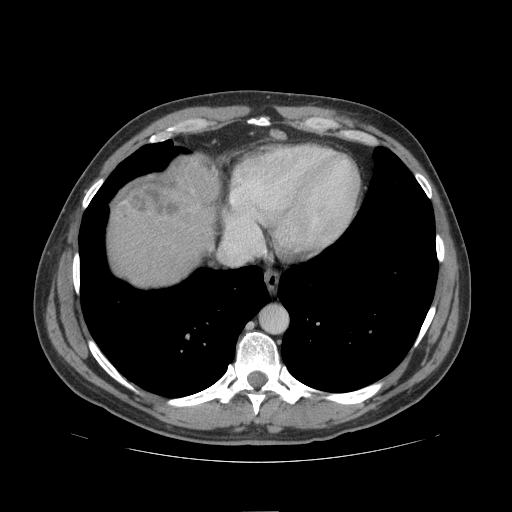
Contrast-enhanced abdominal CT (liver protocol), one axial slice; slice 94 of 109 in the series (ordered by position); reconstruction kernel STANDARD; soft-tissue window (W 400 / L 40 HU); 2.5 mm slice thickness; 512 × 512 image matrix, field of view 420 × 420 mm. Case-level facts recorded for this patient, not image findings: diagnosis: hepatocellular carcinoma (patient treated with transarterial chemoembolisation; whether this scan precedes or follows treatment is not stated here); TNM stage (as recorded): Stage-IIIB; Child-Pugh class: A.
Structures marked on this image (semi-automatic segmentation, software-assisted and operator-edited):
- liver parenchyma outside the tumour (the mass and vessels are separate outlines, so this box may not span the whole liver): bounding box [x1, y1, x2, y2] px = [108, 156, 218, 286]
- mass: [114, 155, 220, 221]